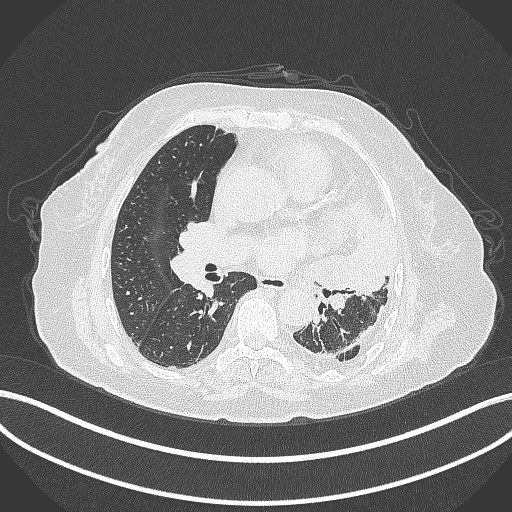
Chest CT, one axial slice. Position 191 of 399 along the scan axis. 120 kVp. Lung window (W 1500 / L -600 HU). 1 mm slice thickness. 512 × 512 image matrix, field of view 400 × 400 mm. Female patient, age 75 years. Case-level facts recorded for this patient, not image findings: clinical TNM (as recorded): T3 N3 M1.
Outlined on this slice (rectangle marked by the reading radiologist):
- lung tumour (recorded histology: adenocarcinoma): bounding box [x1, y1, x2, y2] px = [305, 204, 402, 301]